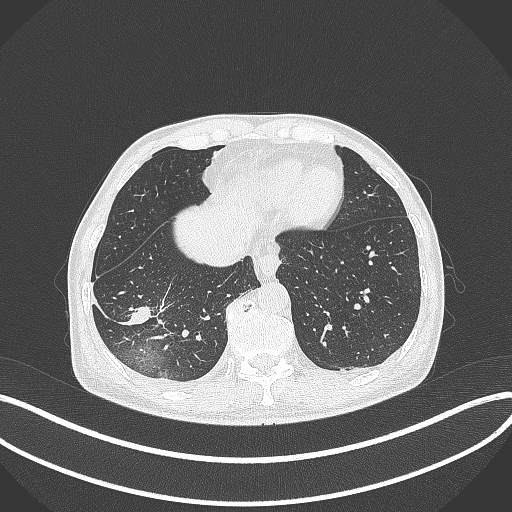
Chest CT, one axial slice. Position 92 of 388 along the scan axis. Lung window (W 1500 / L -600 HU). 1 mm slice thickness. 512 × 512 image matrix, field of view 400 × 400 mm. Male patient, age 64 years. From the clinical record (not read from this slice): clinical TNM (as recorded): T3 N0 M0; histopathological grade: G2-3.
Annotated regions visible in this slice (bounding box drawn by a radiologist):
- lung tumour (recorded histology: adenocarcinoma): bounding box <113,300,149,327> (left, top, right, bottom; pixels)